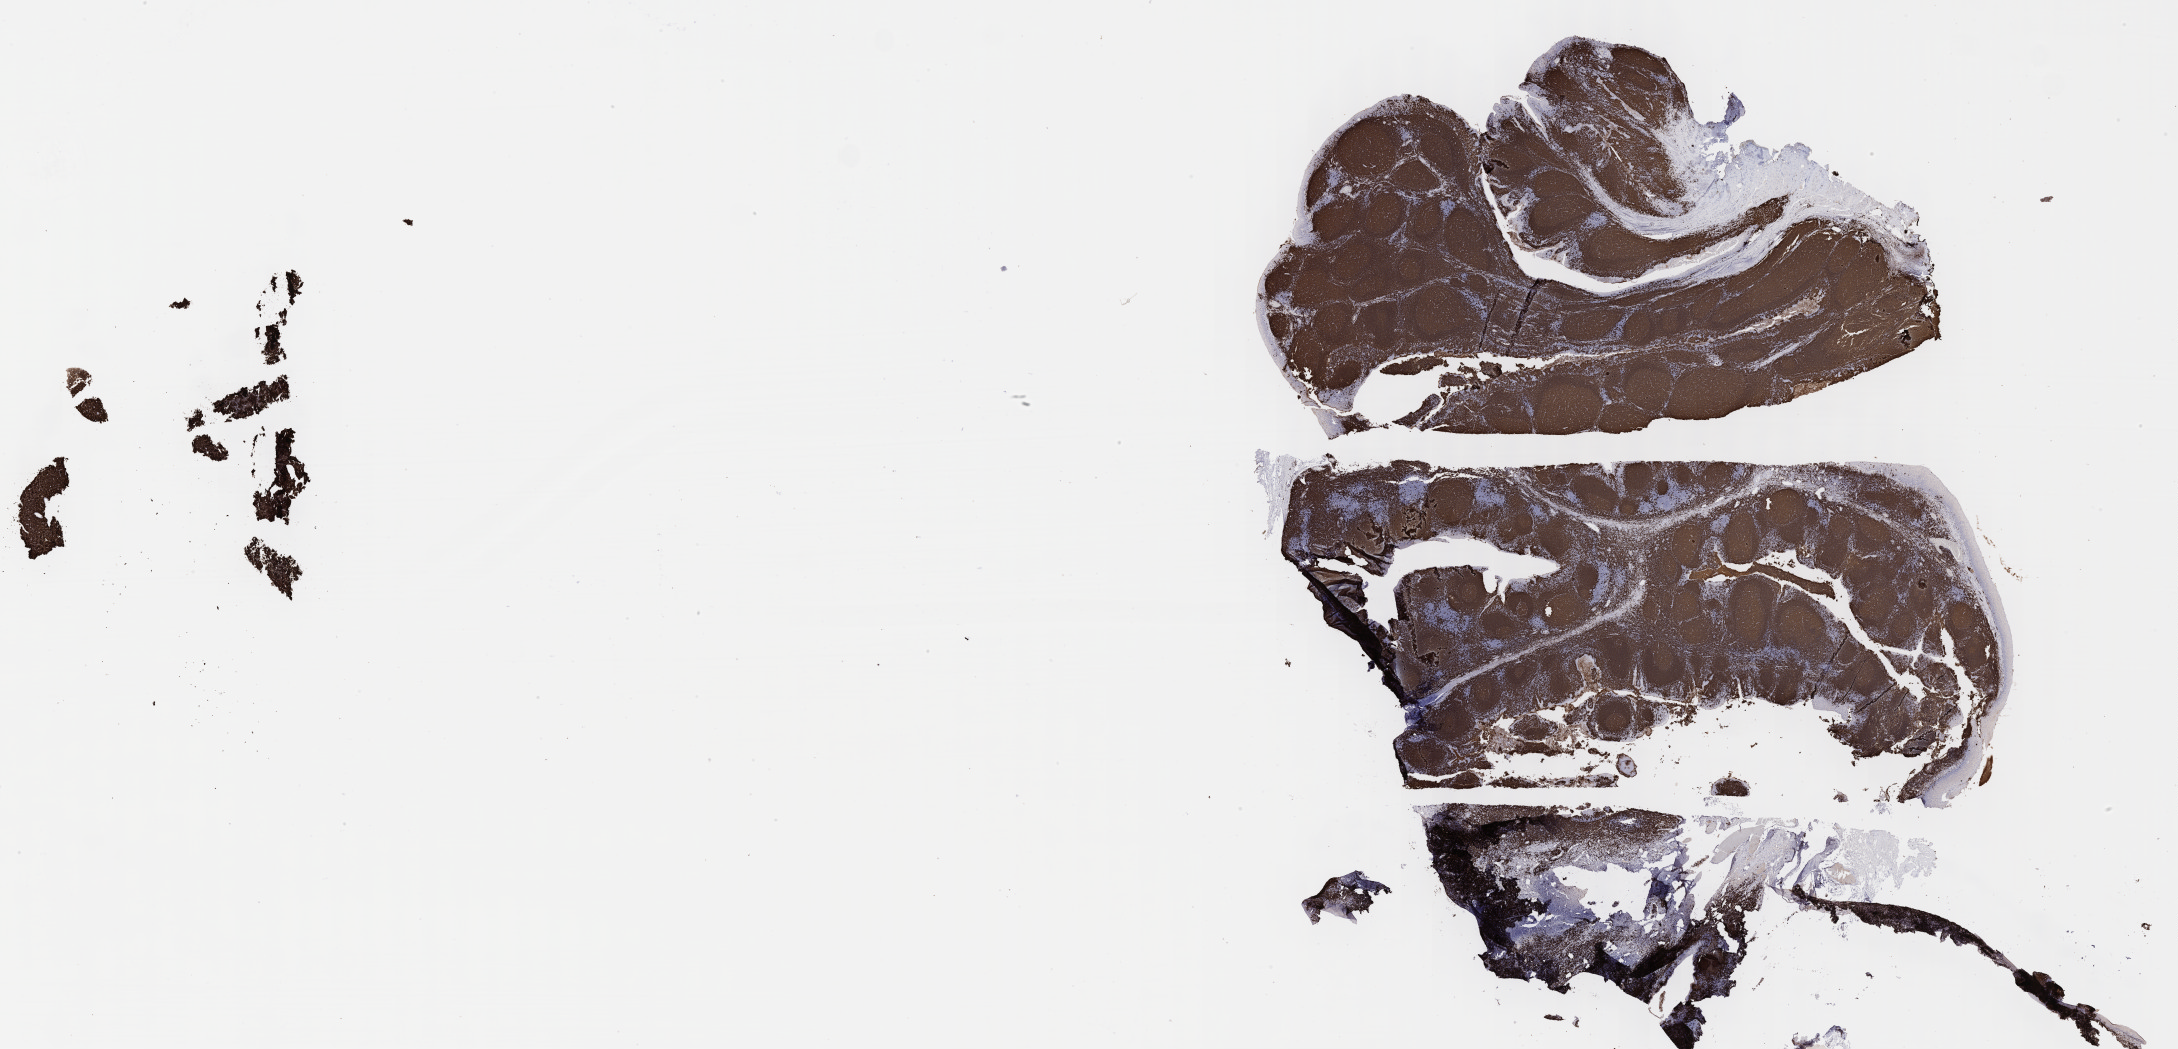
Immunohistochemistry (IHC) whole-slide image stained for CD20, shown as a low-resolution overview of the whole scanned area (about 35.2 x 17.0 mm); specimen: tumor tissue; site: peritoneum. Patient: female, age at initial diagnosis 6 years.
* histologic diagnosis: Burkitt lymphoma, NOS